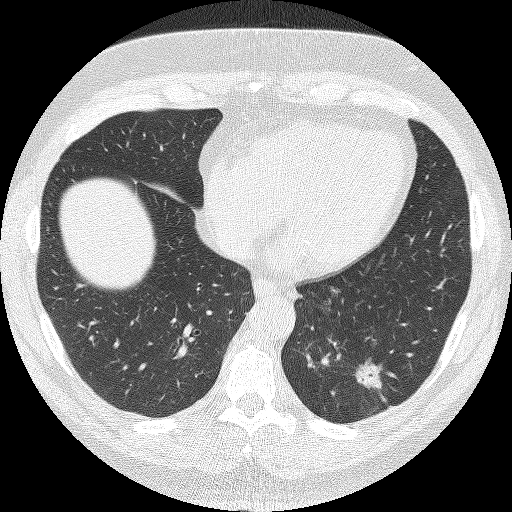
Low-dose screening chest CT, axial slice. First (baseline) screen. Lung window (W 1500 / L -600 HU). Lung (sharp) reconstruction kernel (FC51). 512 × 512 image matrix. Male participant, aged 62 years at enrolment. Current smoker at enrolment.
• Expert reader's lesion annotation, bounding box [x1, y1, x2, y2] px = [348, 353, 405, 403].
• The screening reader recorded 2 non-calcified nodules or masses ≥4 mm on this exam (left lower lobe, right upper lobe); which of them this box marks is not recorded.